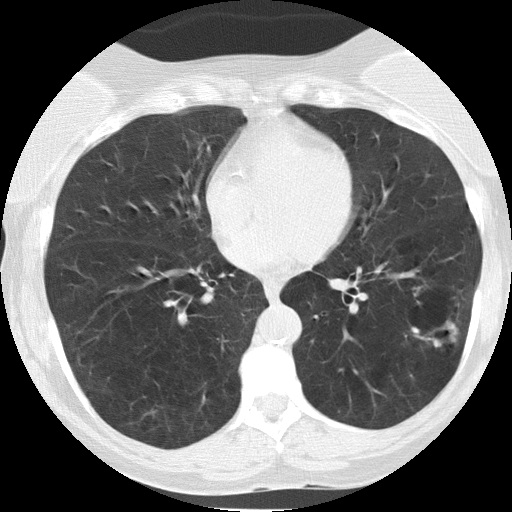
Axial slice from a low-dose chest CT screening exam; baseline annual screen; lung window (W 1500 / L -600 HU); lung (sharp) reconstruction kernel (FC51); slice 84 of 149 in the series. Female participant, aged 58 years at enrolment. Current smoker at enrolment.
Expert-annotated lung lesion, box from (x=403, y=310) to (x=459, y=351) px. The screening reader recorded 3 non-calcified nodules or masses ≥4 mm on this exam (right lower lobe, lingula, left lower lobe); which of them this box marks is not recorded. Participant outcome: lung cancer diagnosed 93 days after this screen — adenocarcinoma, NOS, left lower lobe, moderately differentiated (G2), stage IIIB (AJCC 6th edition), 14 mm at pathology.